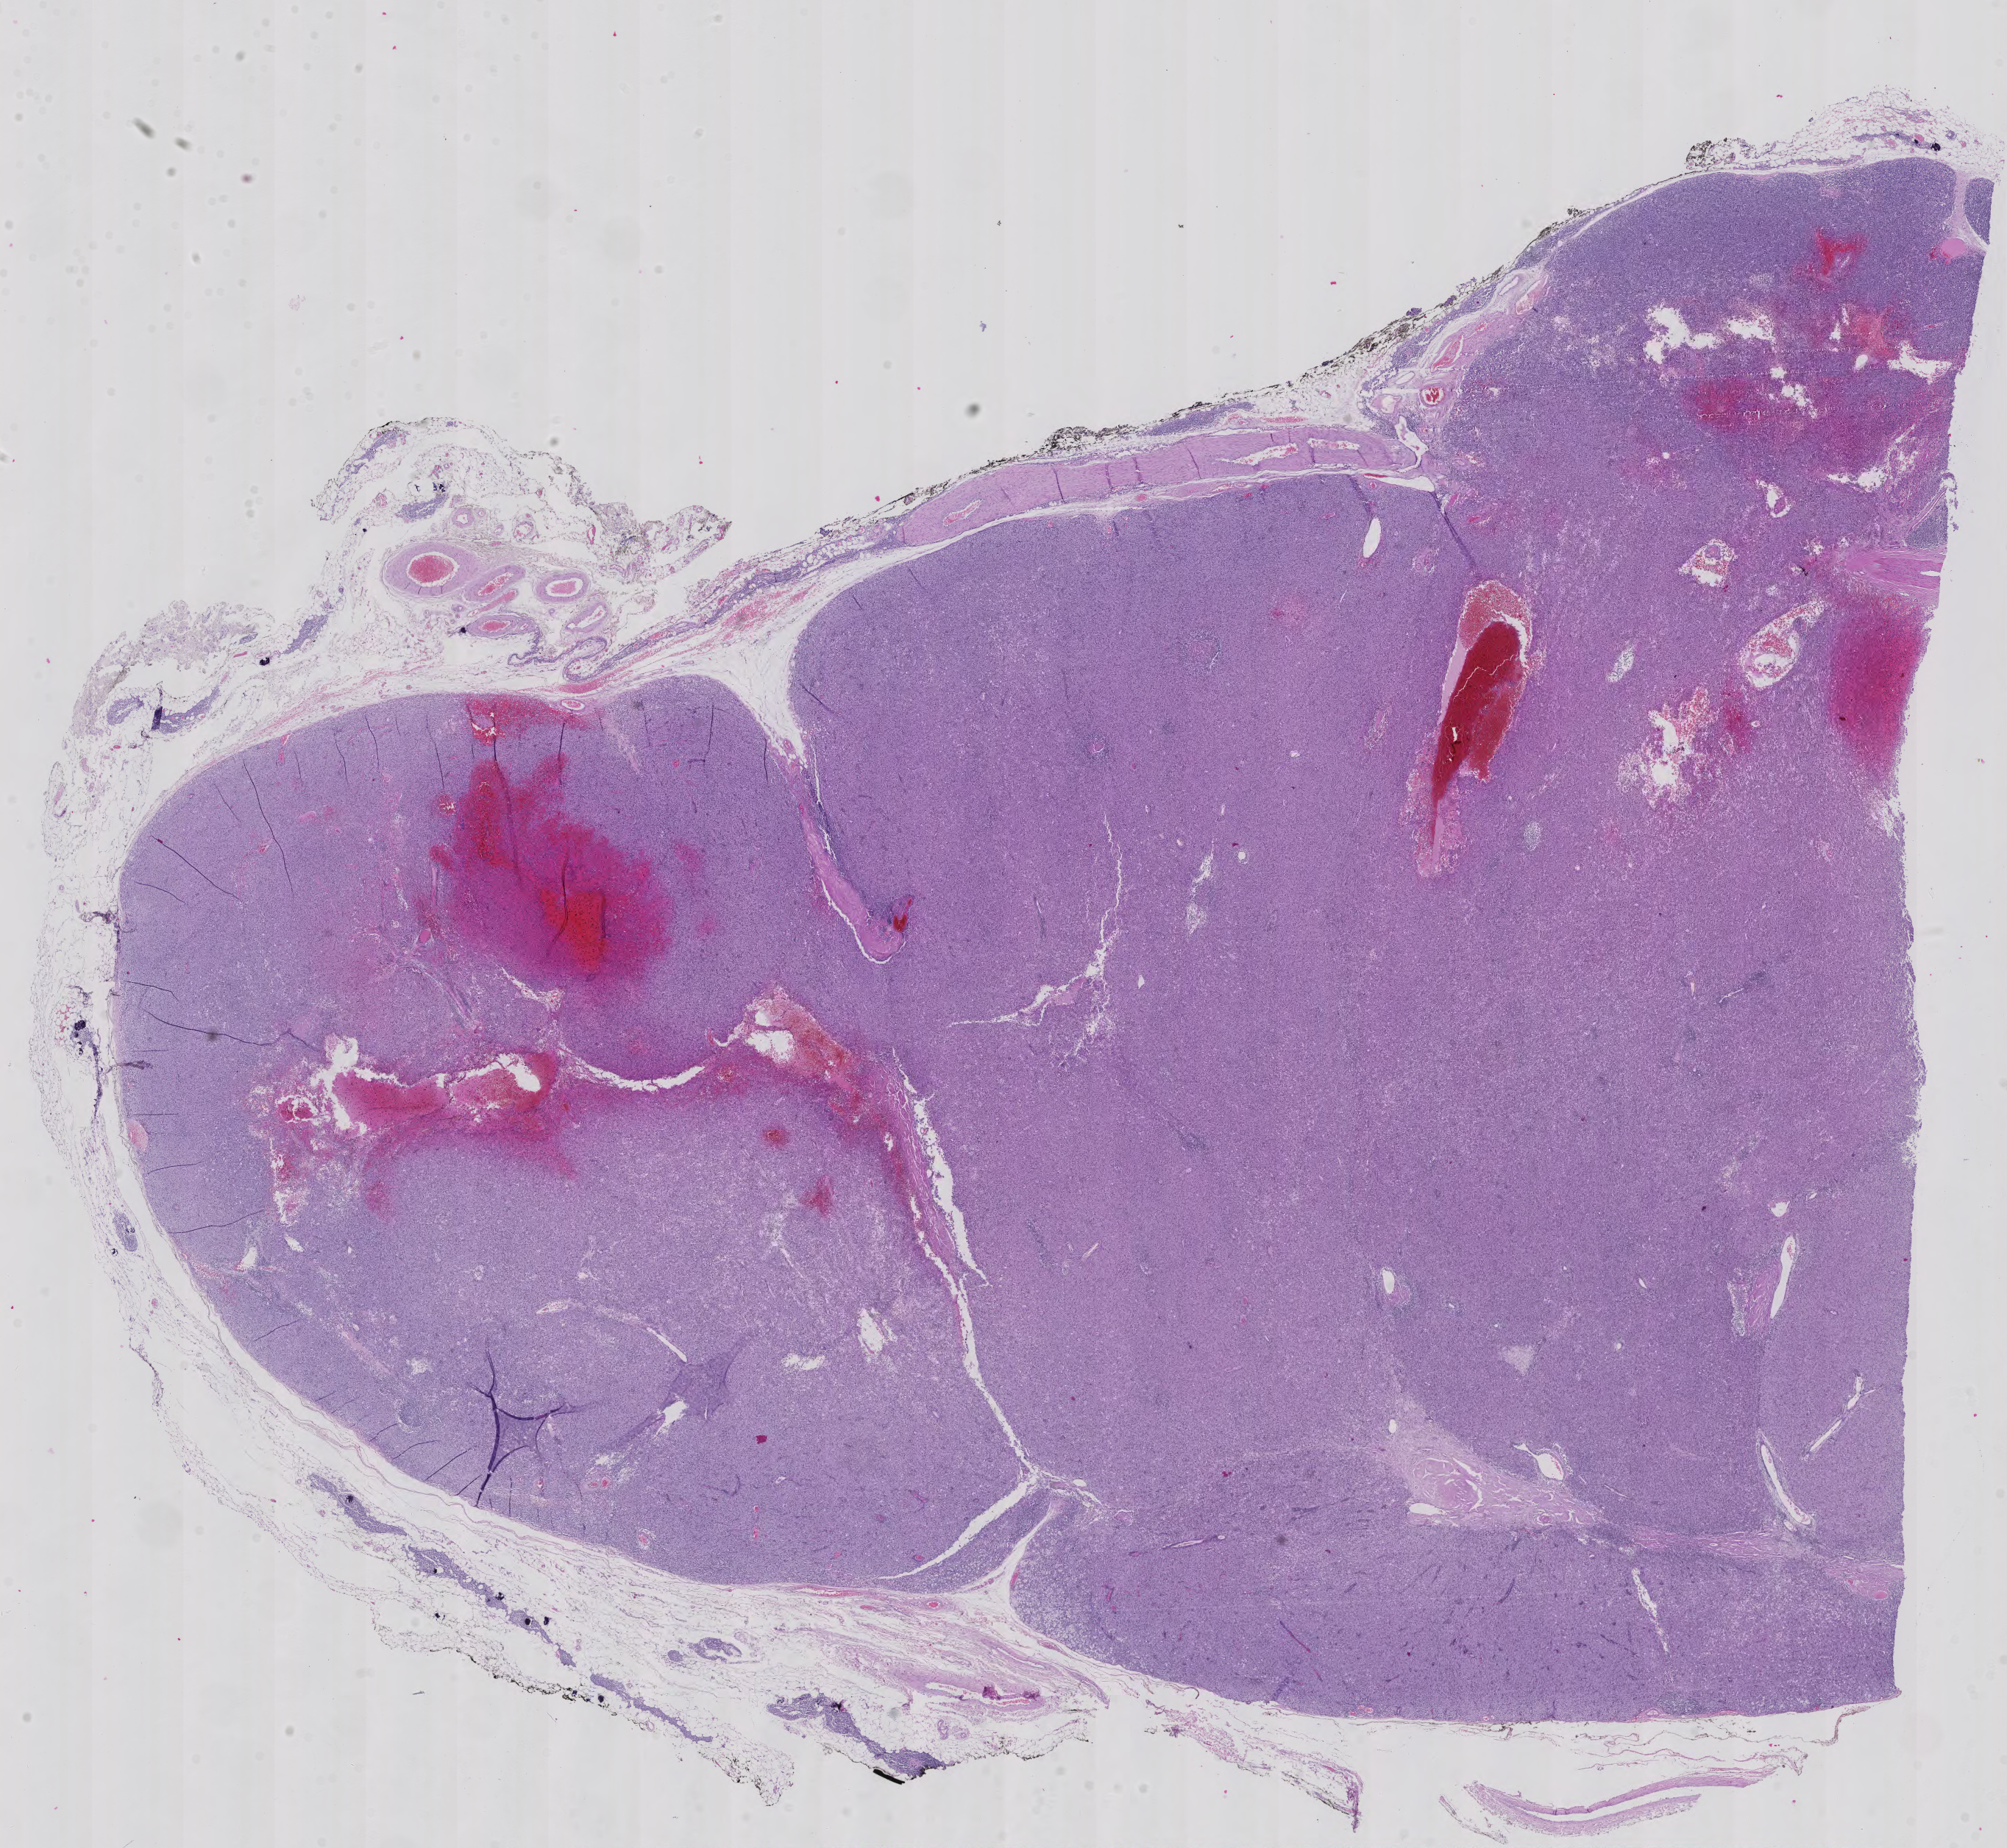
Digitized H&E tissue section (whole slide), shown as a low-resolution overview of the whole scanned area (about 19.9 x 18.3 mm), formalin-fixed paraffin-embedded (FFPE) diagnostic section, primary tumour sample from the thymus. Male, age 69 years at initial diagnosis.
Diagnosis: Thymoma, type A, malignant (anterior mediastinum).